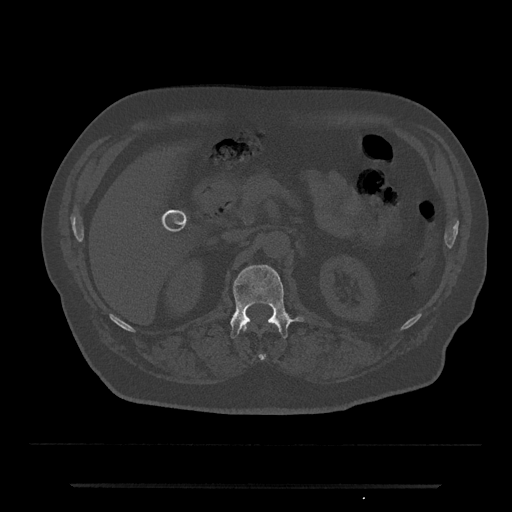
CT including the spine, one axial slice. Position 549 of 797 along the scan axis. Reconstruction kernel Br40s/3. 120 kVp. Bone window (W 1800 / L 400 HU). 0.5 mm slice thickness. 512 × 512 image matrix. Male patient, age 80 years. From the clinical record (not read from this slice): primary cancer: prostate; vertebrae with lytic lesions (as recorded): L1, T11.
Structures marked on this image (semi-automatic segmentation, software-assisted and operator-edited):
- L1 vertebra: bounding box [x1, y1, x2, y2] px = [230, 265, 305, 338]
- T12 vertebra: [242, 326, 278, 360]